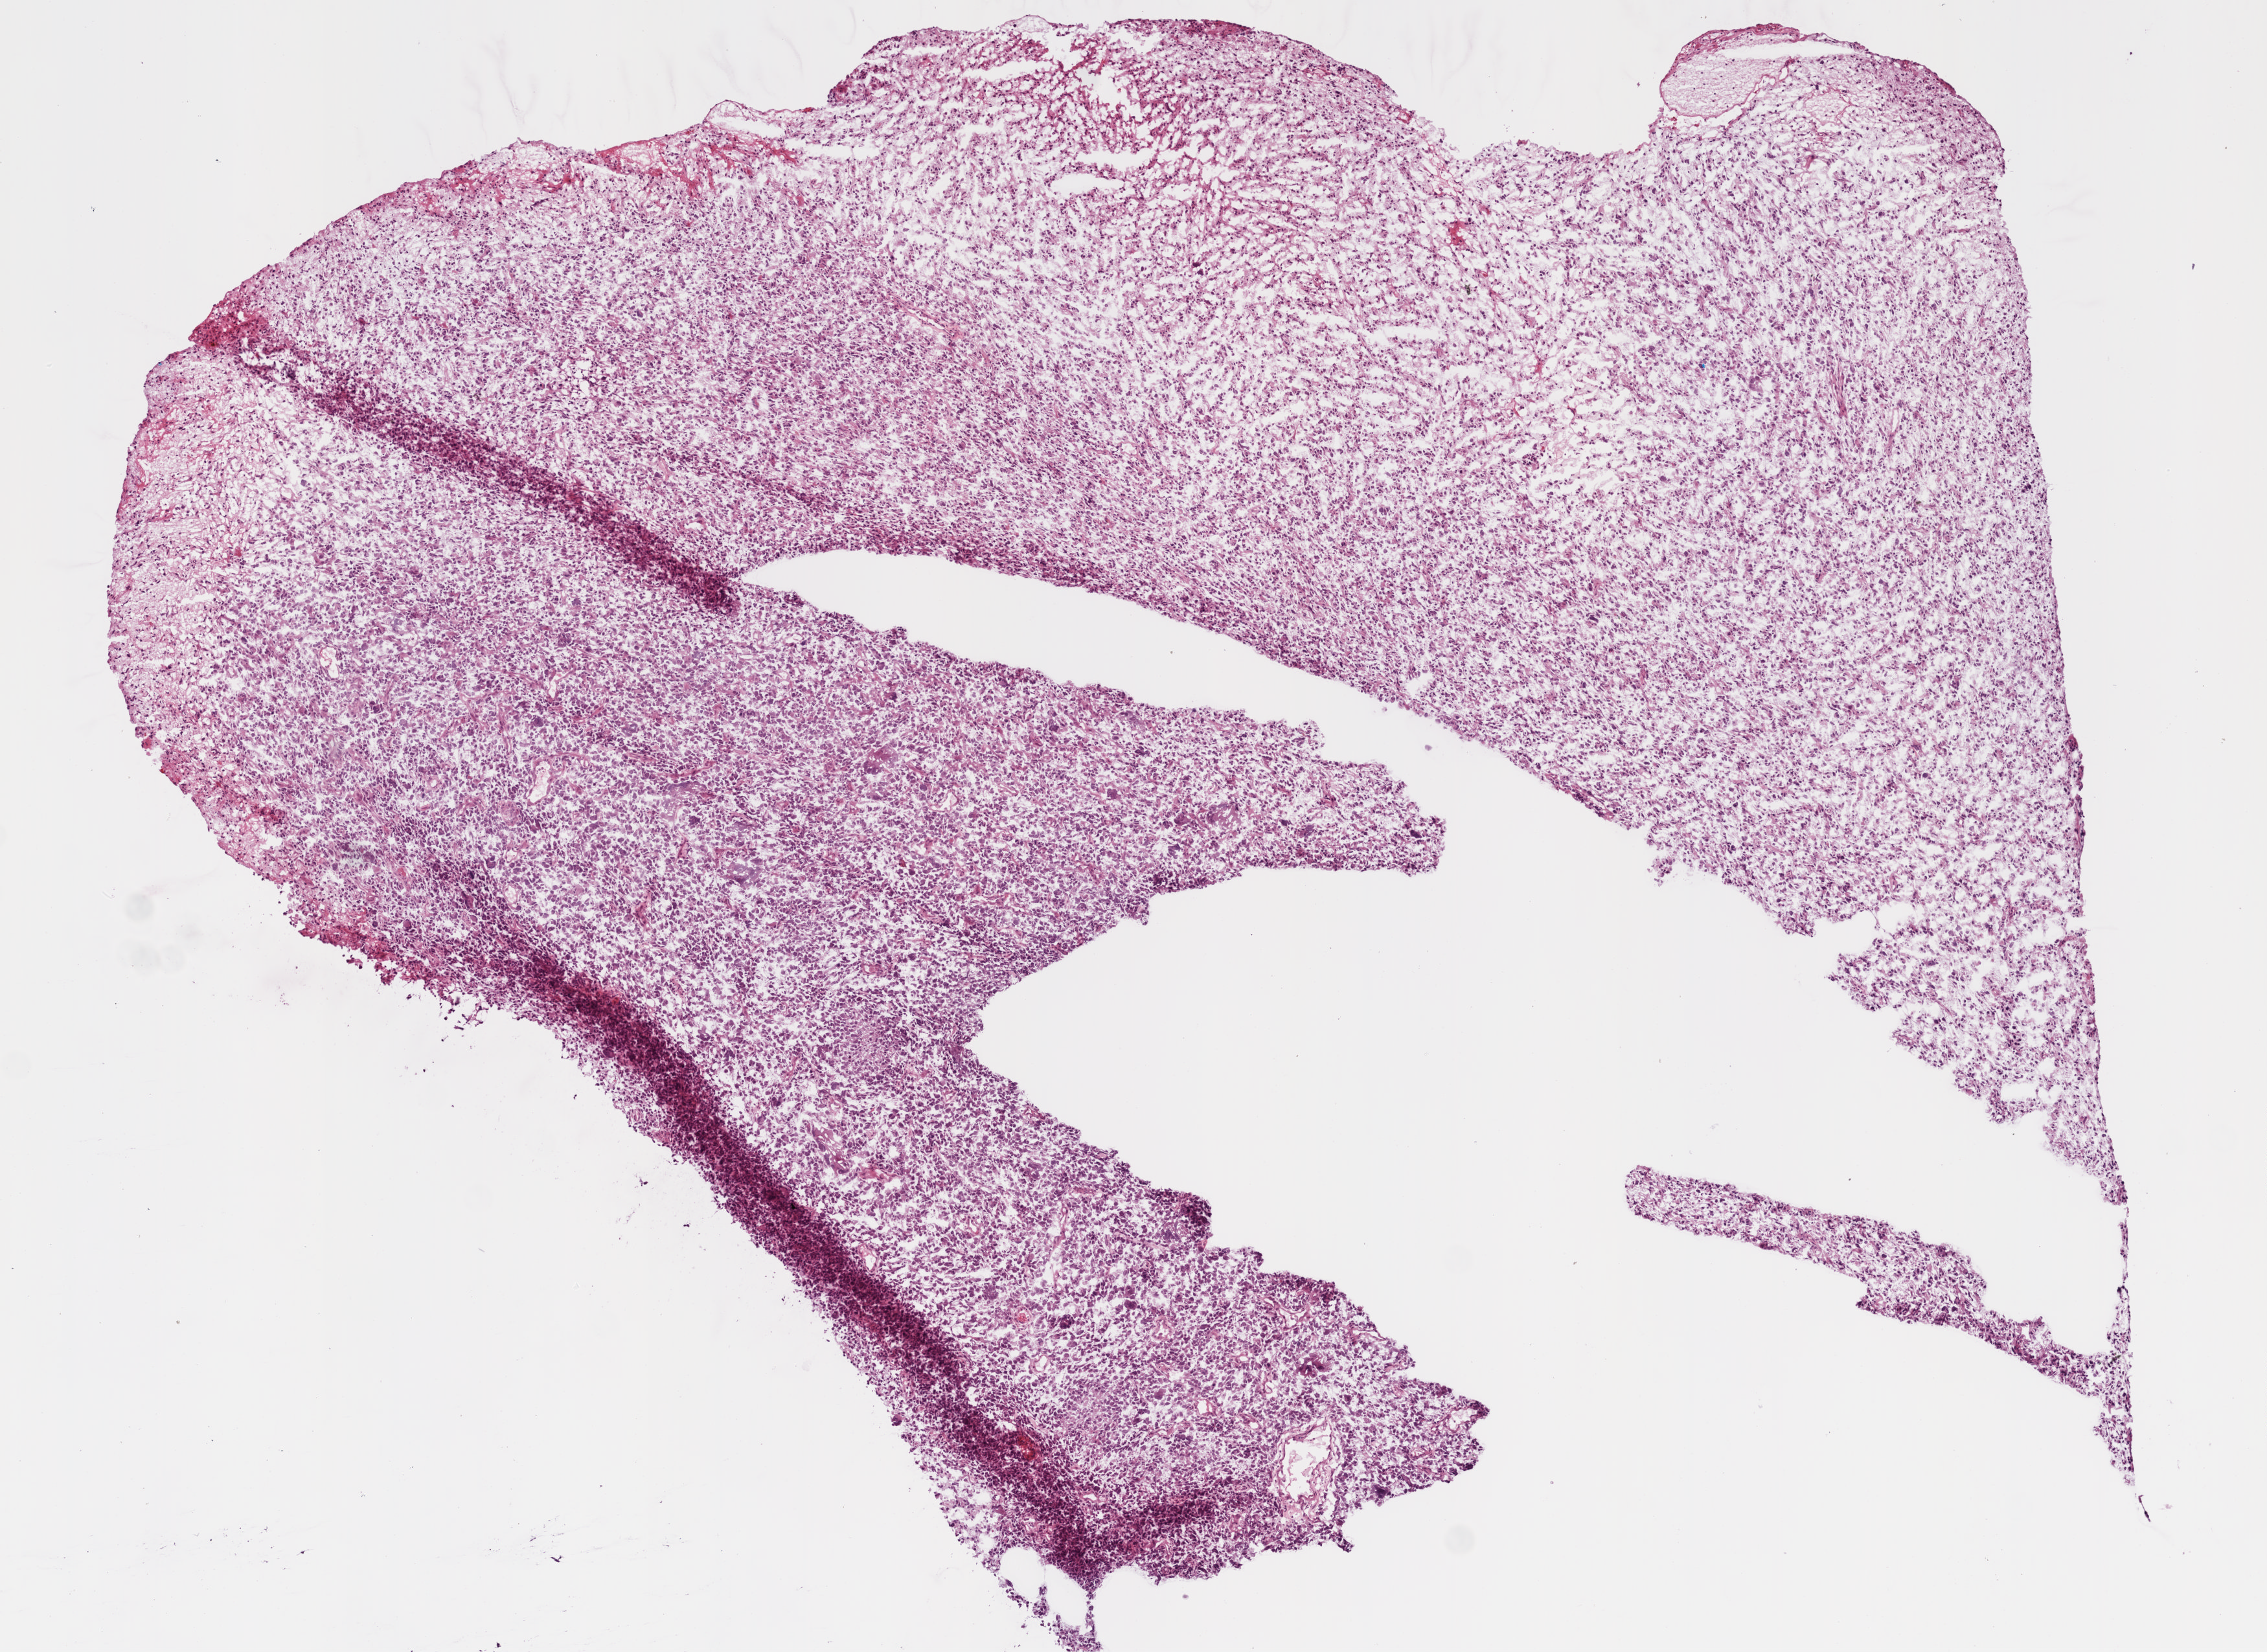
Digitized Hematoxylin and eosin (H&E) stained tissue section (whole slide) — whole scanned area (about 7.0 x 5.1 mm) shown as a low-resolution overview; frozen section from the bottom of the tissue portion; sample: primary tumour, brain. Male patient; age at initial diagnosis 86 years. Slide review estimates, as recorded: tumour cells 90%, tumour nuclei 90%, normal cells 0%, stromal cells 10%, necrosis 0%.
* pathologic diagnosis: Glioblastoma